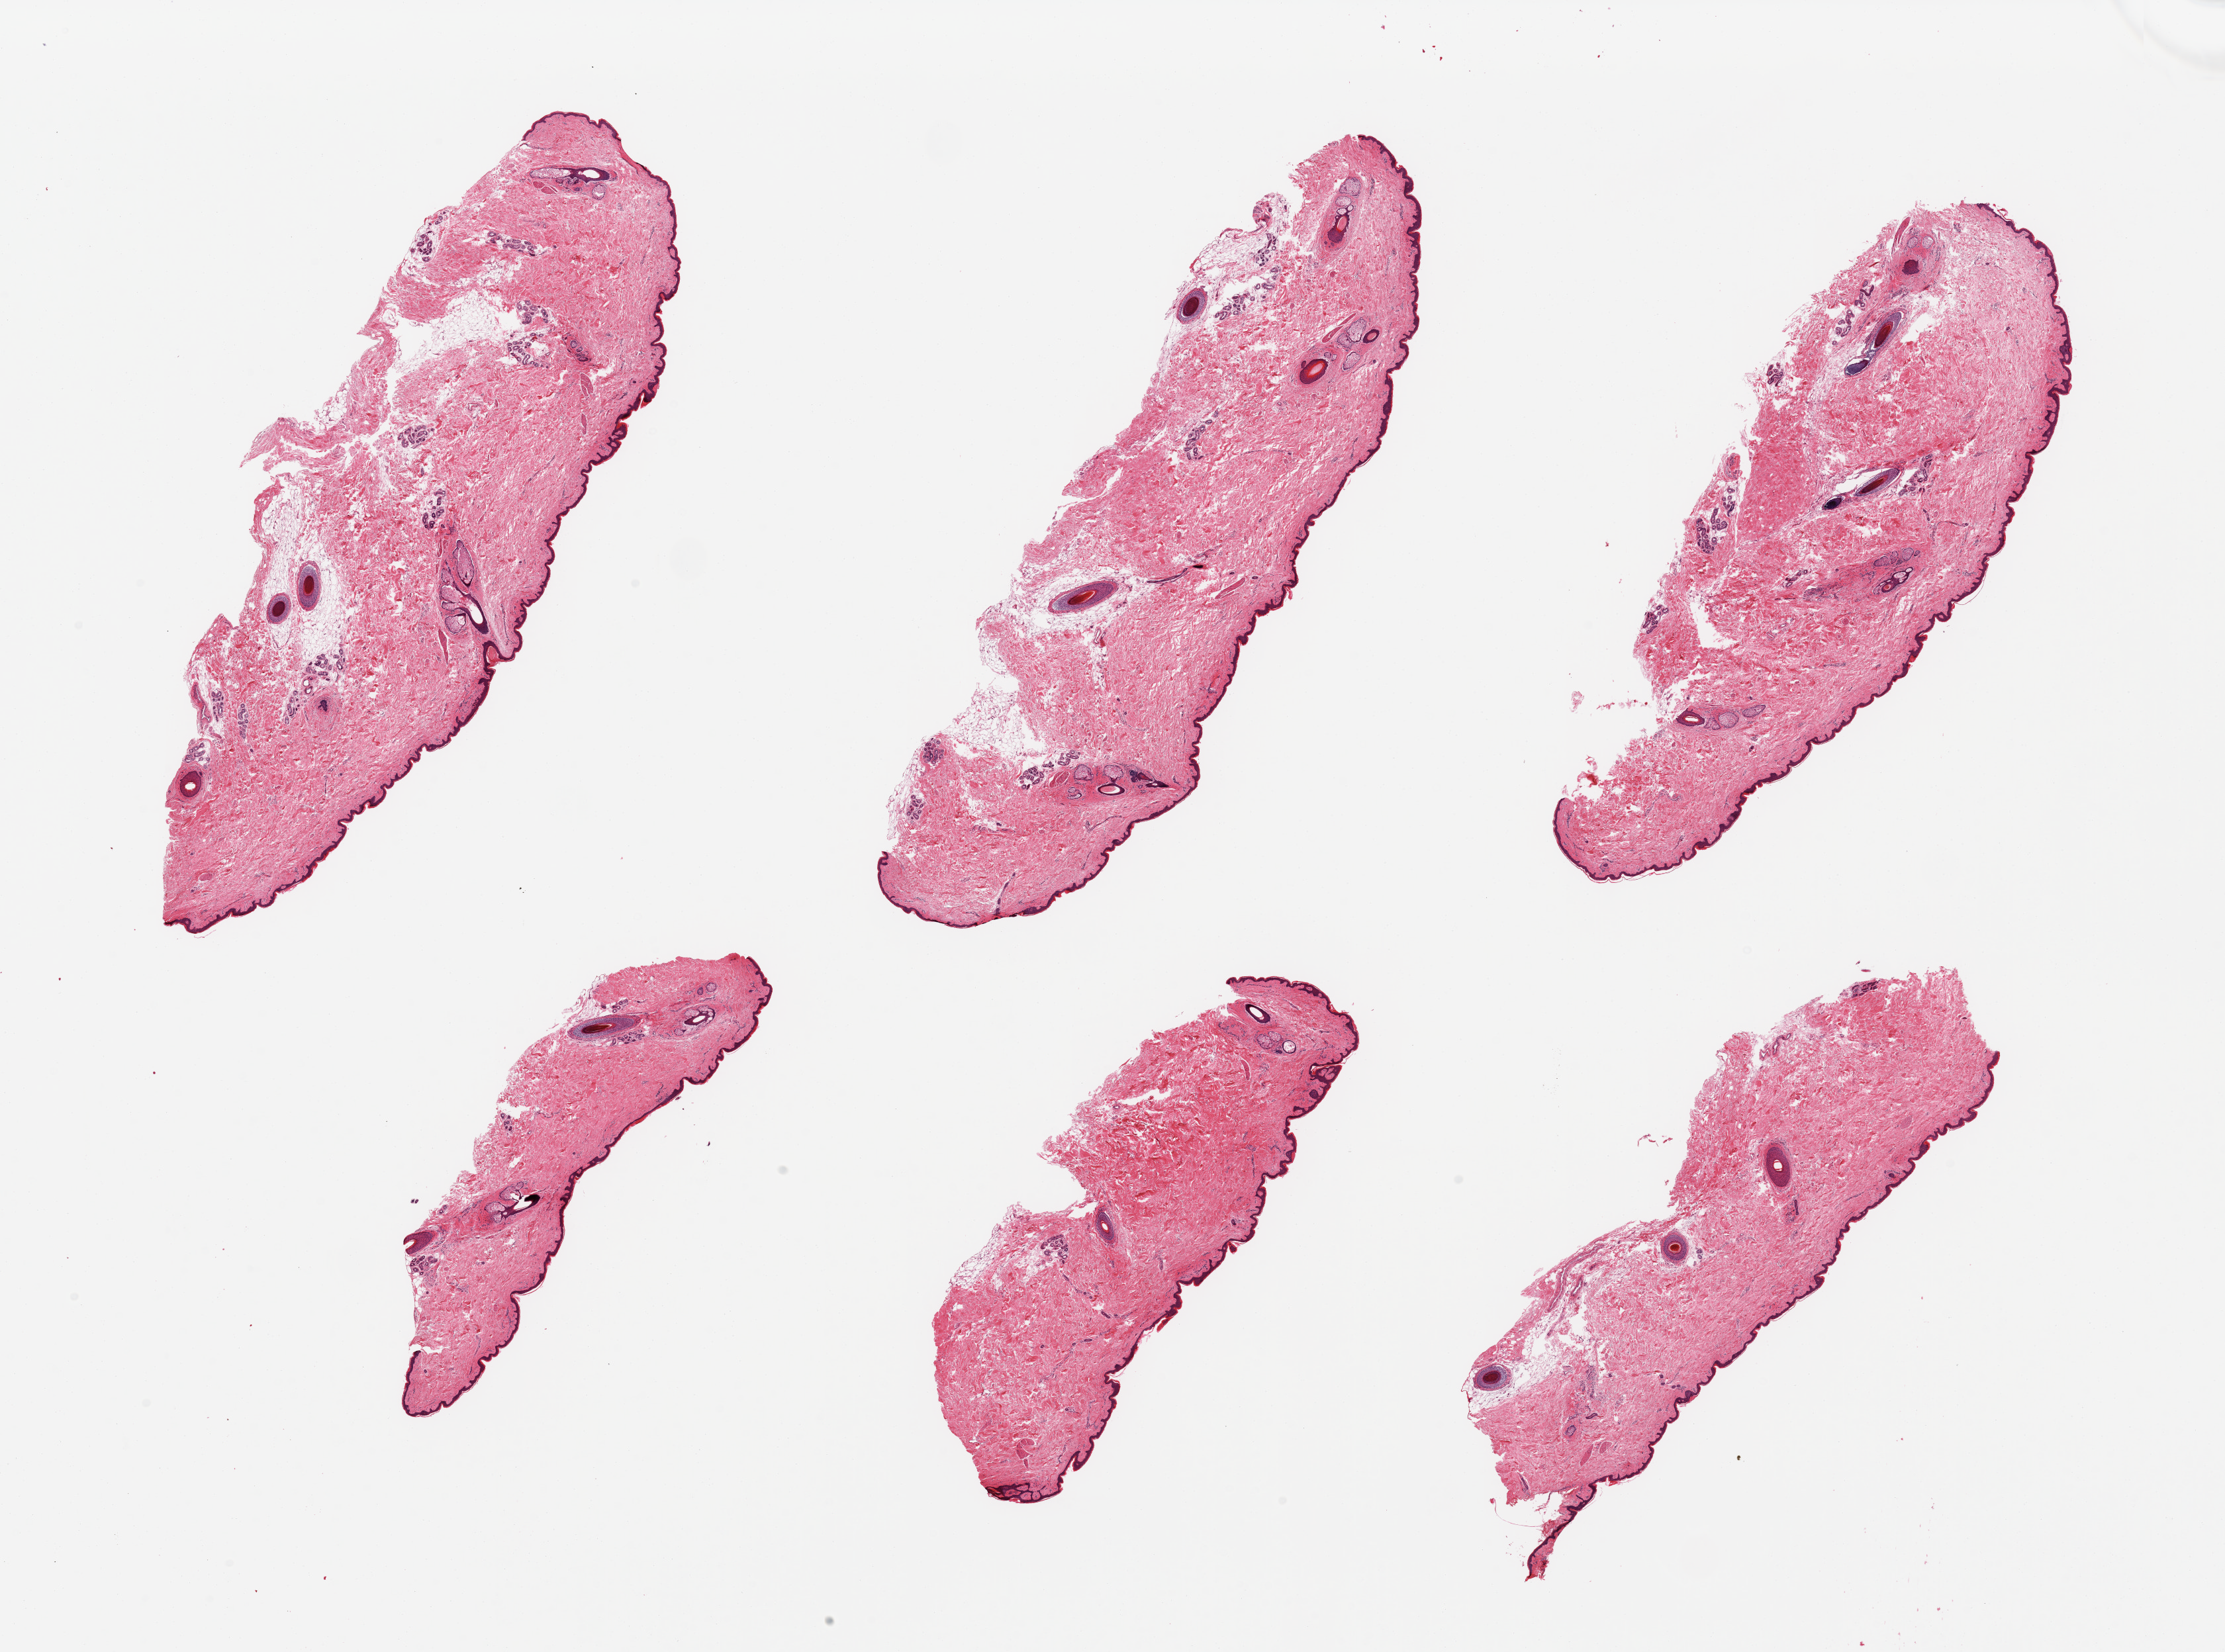
Digitized hematoxylin and eosin (H&E)-stained section, whole scanned area (about 26.6 x 19.7 mm) shown as a low-resolution overview, PAXgene-fixed paraffin-embedded (PFPE) section, section of skin of suprapubic region (target tissue), donor tissue sample. Donor: male.
Review note (as recorded): 6 pieces; well trimmed; 10% dermal fat; several hair follicles.